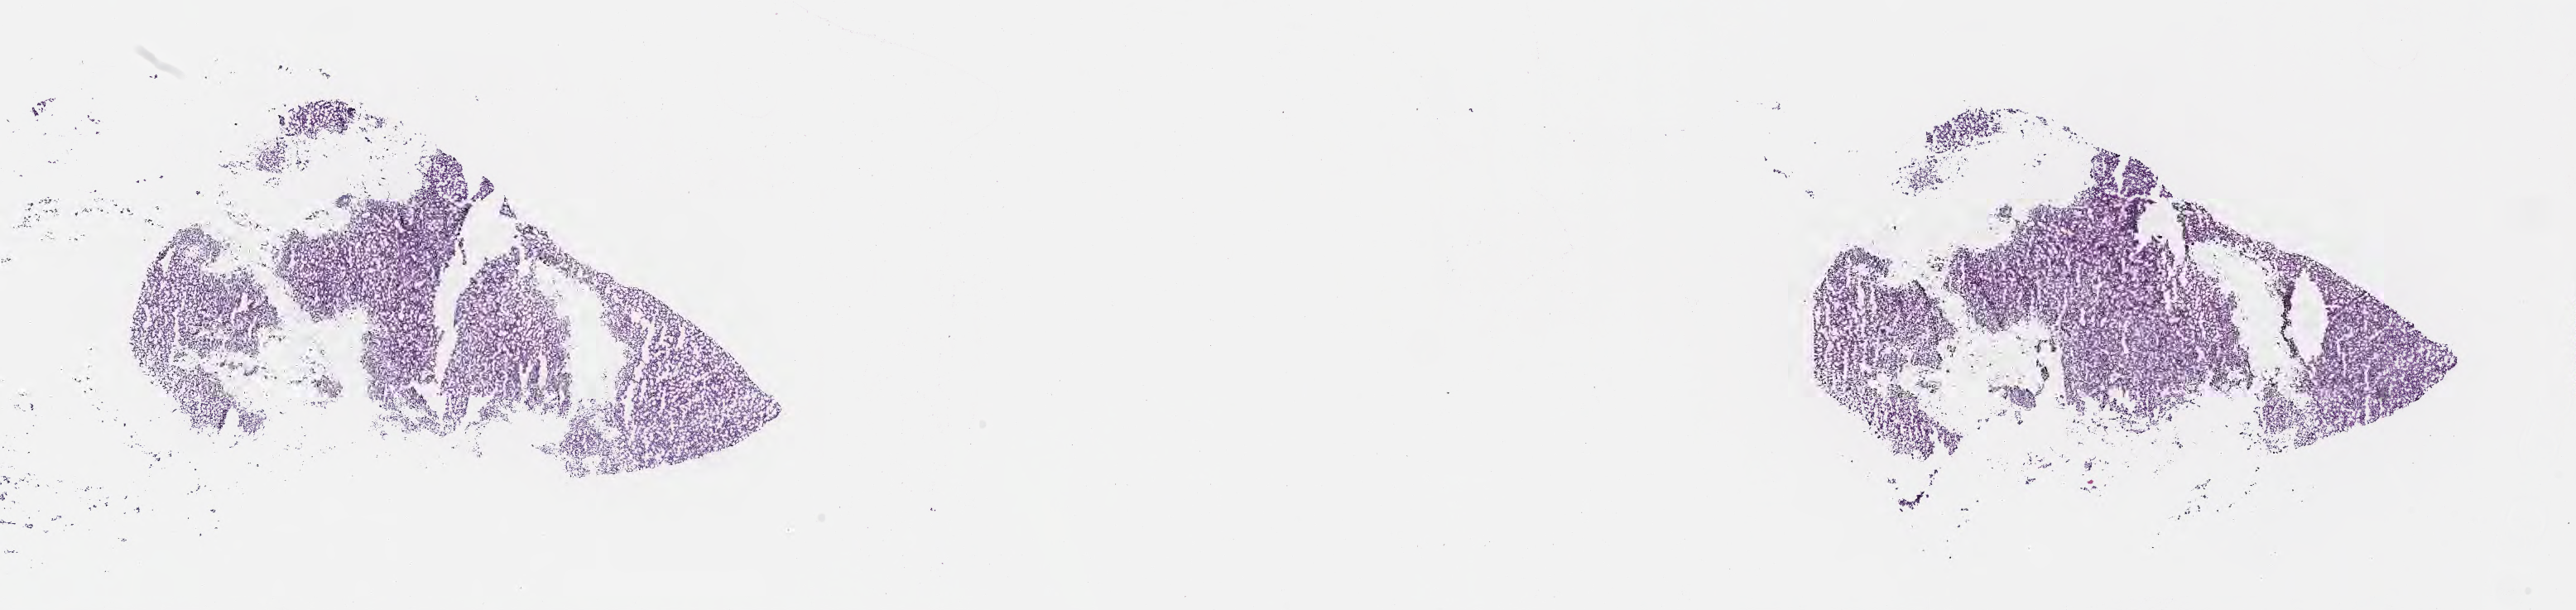
Digitized haematoxylin and eosin-stained section, shown as a low-resolution overview of the whole scanned area (about 25.2 x 6.0 mm); cryosection; primary tumor; site: liver. Male patient; age at initial diagnosis 86 years. Tumor grade: G3 (poorly differentiated). Composition of this section per pathologist review: tumor cells 80%, tumor nuclei 80%, stromal cells 20%, necrosis 0%, normal cells 0%. Inflammatory infiltration, as recorded: lymphocyte infiltration 0%, monocyte infiltration 0%, neutrophil infiltration 0%.
• AJCC pathologic stage: Stage IIIB
• section: bottom of the tissue portion
• diagnosis: Hepatocellular carcinoma, NOS